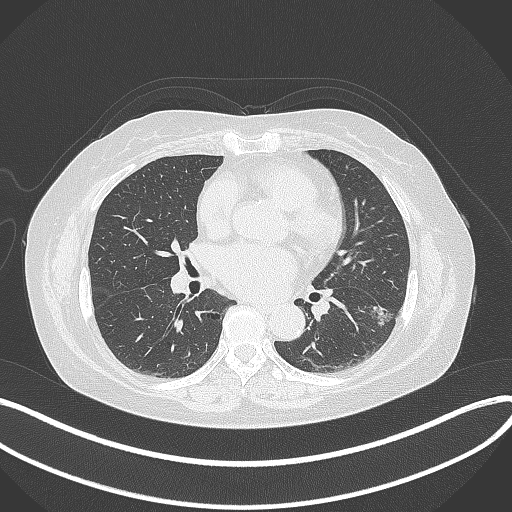
Chest CT, one axial slice; reconstruction kernel B70f; 120 kVp; lung window (W 1500 / L -600 HU); 1 mm slice thickness; 512 × 512 image matrix, field of view 400 × 400 mm. Female patient, age 67 years. From the clinical record (not read from this slice): clinical TNM (as recorded): T1c N0 M0.
Annotated regions visible in this slice (rectangle marked by the reading radiologist):
- lung tumour (recorded histology: adenocarcinoma): bounding box <362,296,396,328> (left, top, right, bottom; pixels)